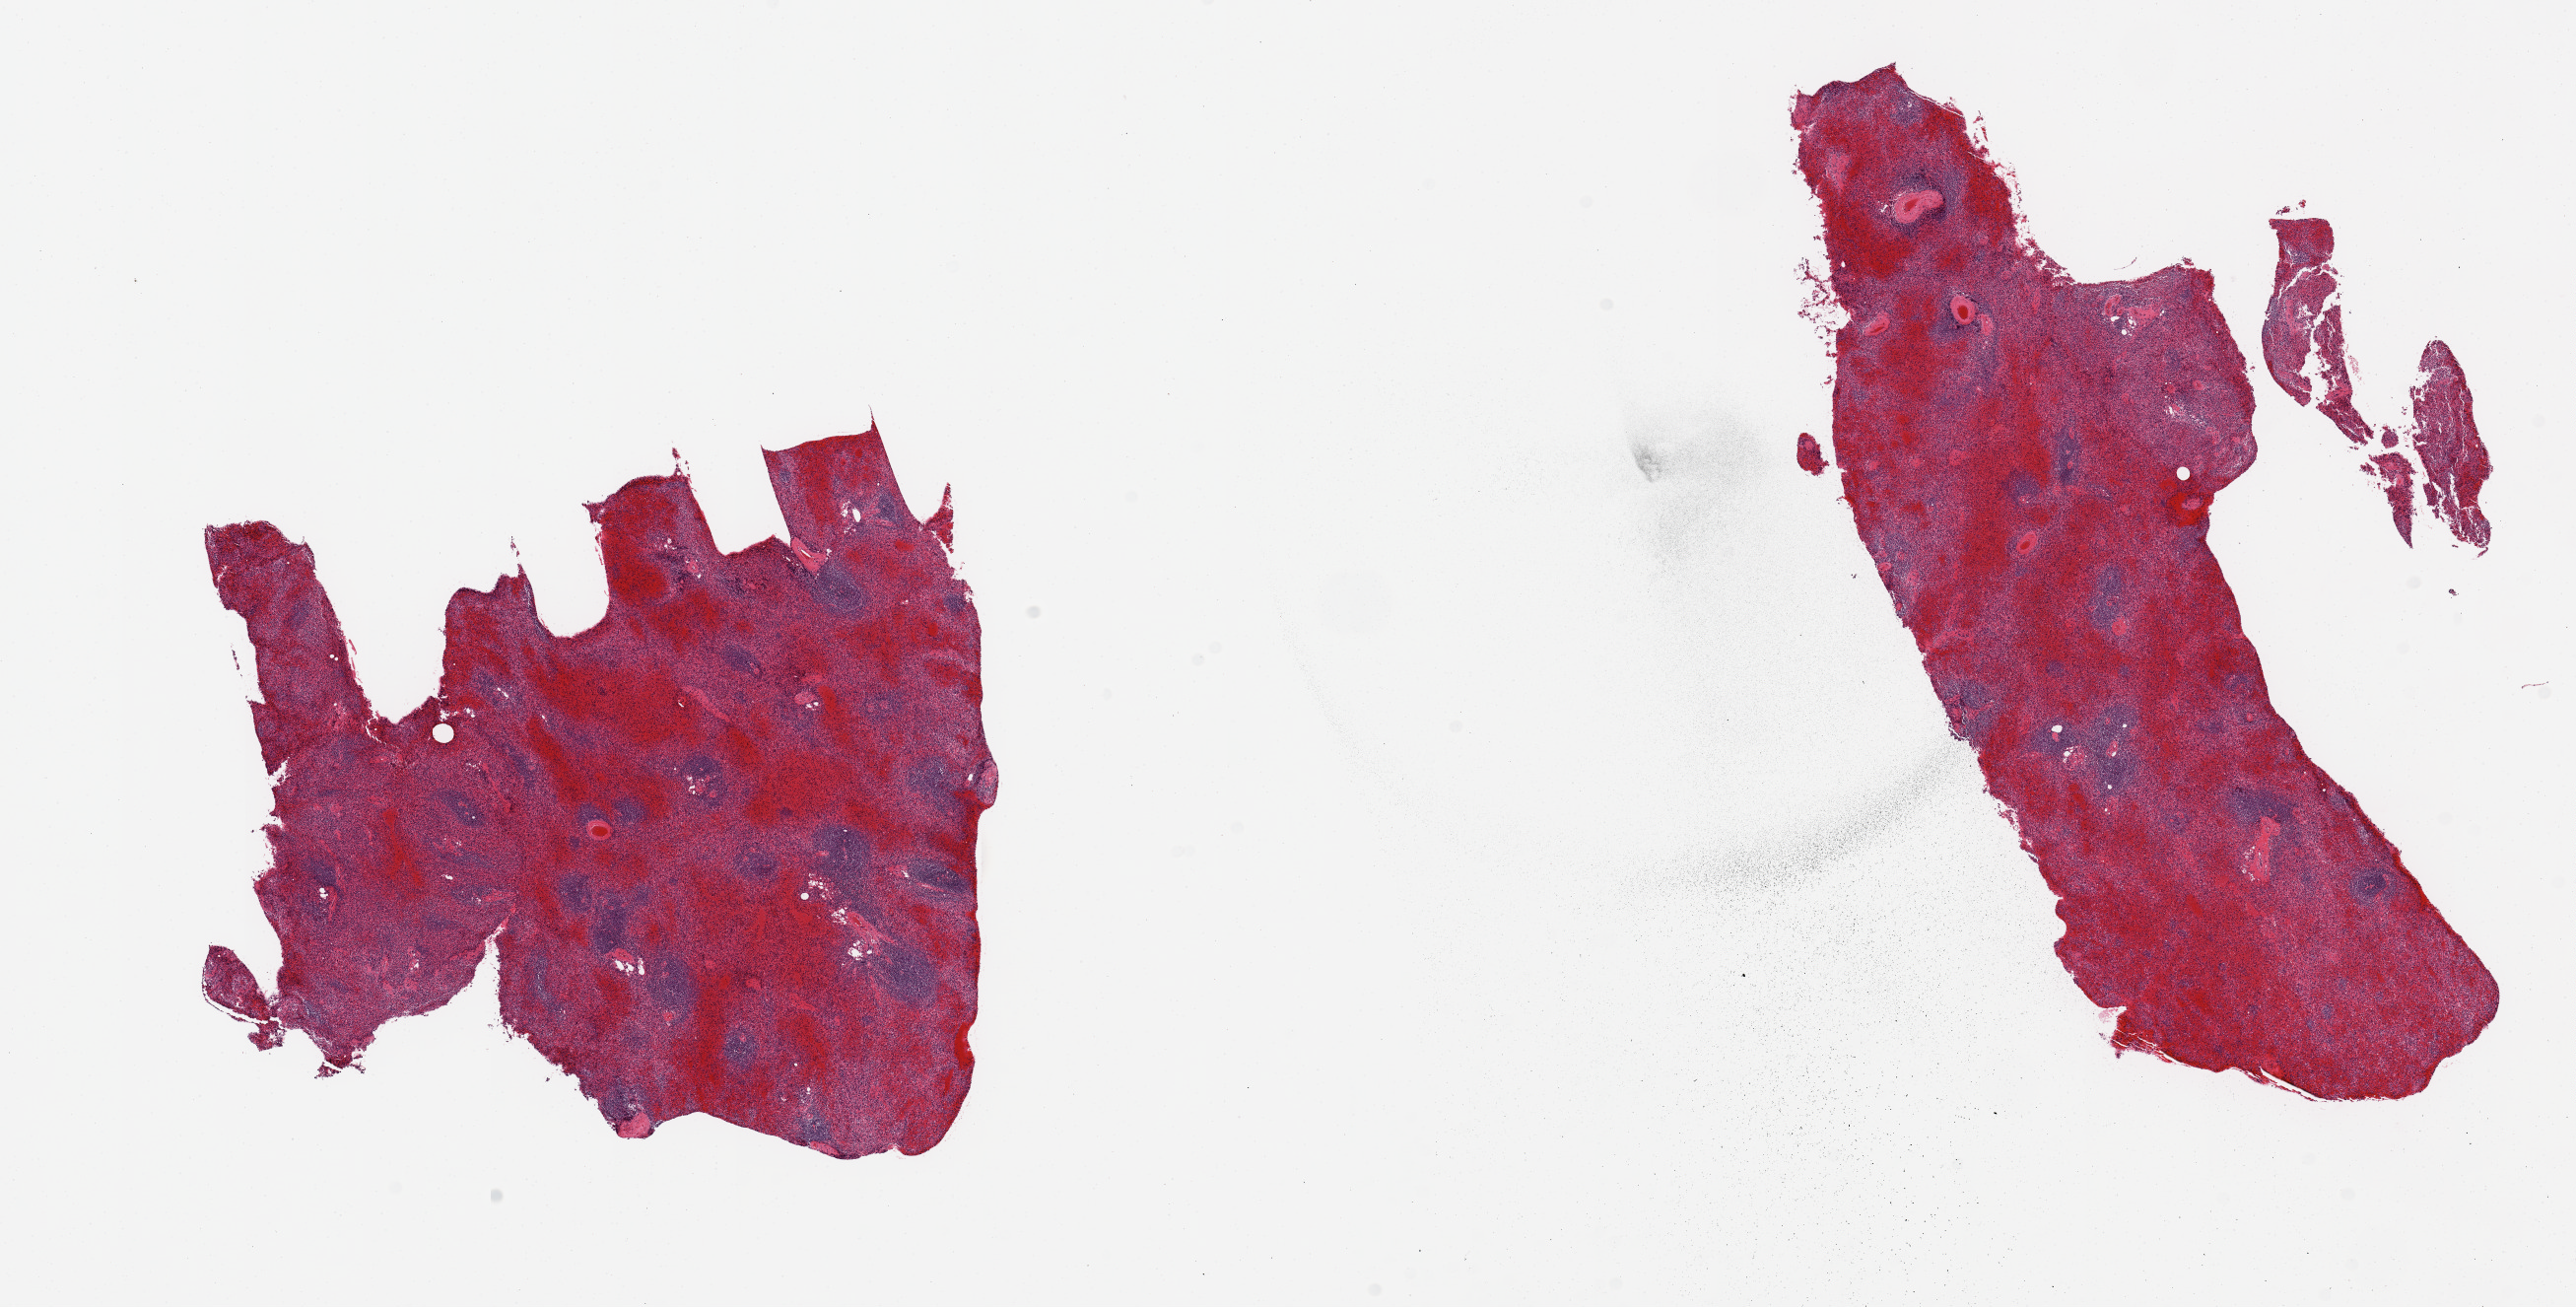
Digitized haematoxylin and eosin-stained section, whole scanned area (about 20.7 x 10.5 mm) shown as a low-resolution overview. PAXgene-fixed, paraffin-embedded tissue. Section of spleen (target tissue). Tissue donor sample. Male donor.
* reviewer comment on this tissue sample: 2 pieces, moderate congestion, advanced autolysis